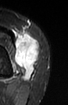
MRI of an extremity soft-tissue mass, one axial slice. Position 26 of 52 along the scan axis. STIR. MR volume resampled by the dataset authors to the PET/CT grid (not the native acquisition matrix). 68 × 105 image matrix, field of view 66 × 103 mm. Female patient. From the clinical record (not read from this slice): histological type: spindle cell suggestive of biphasic synovial sarcoma; grade: intermediate; site of the primary tumour: left knee.
Outlined on this slice (expert contour drawn on MRI and transferred to this co-registered scan by the dataset authors):
- gross tumour volume including surrounding oedema: bounding box <14,31,41,80> (left, top, right, bottom; pixels)
- gross tumour volume (mass): <14,34,41,80>